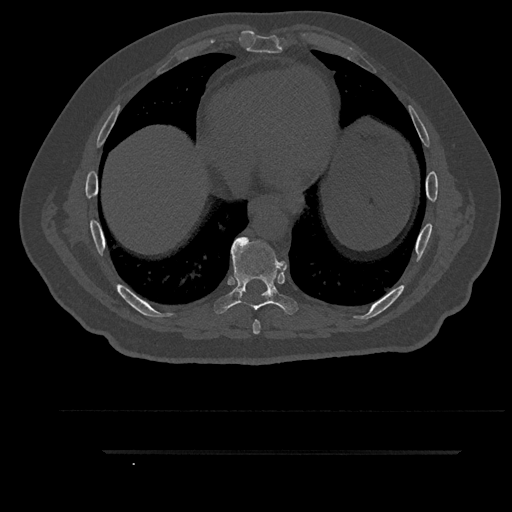
CT including the spine, one axial slice. Position 483 of 797 along the scan axis. Reconstruction kernel Br40s/3. 120 kVp. Bone window (W 1800 / L 400 HU). 0.5 mm slice thickness. 512 × 512 image matrix, field of view 432 × 432 mm. Male patient, age 63 years. From the clinical record (not read from this slice): primary cancer: renal; vertebrae with lytic lesions (as recorded): T8.
Structures marked on this image (semi-automatically segmented with operator editing):
- T7 vertebra: bounding box <242,237,261,334> (left, top, right, bottom; pixels)
- T8 vertebra: <214,237,298,315>